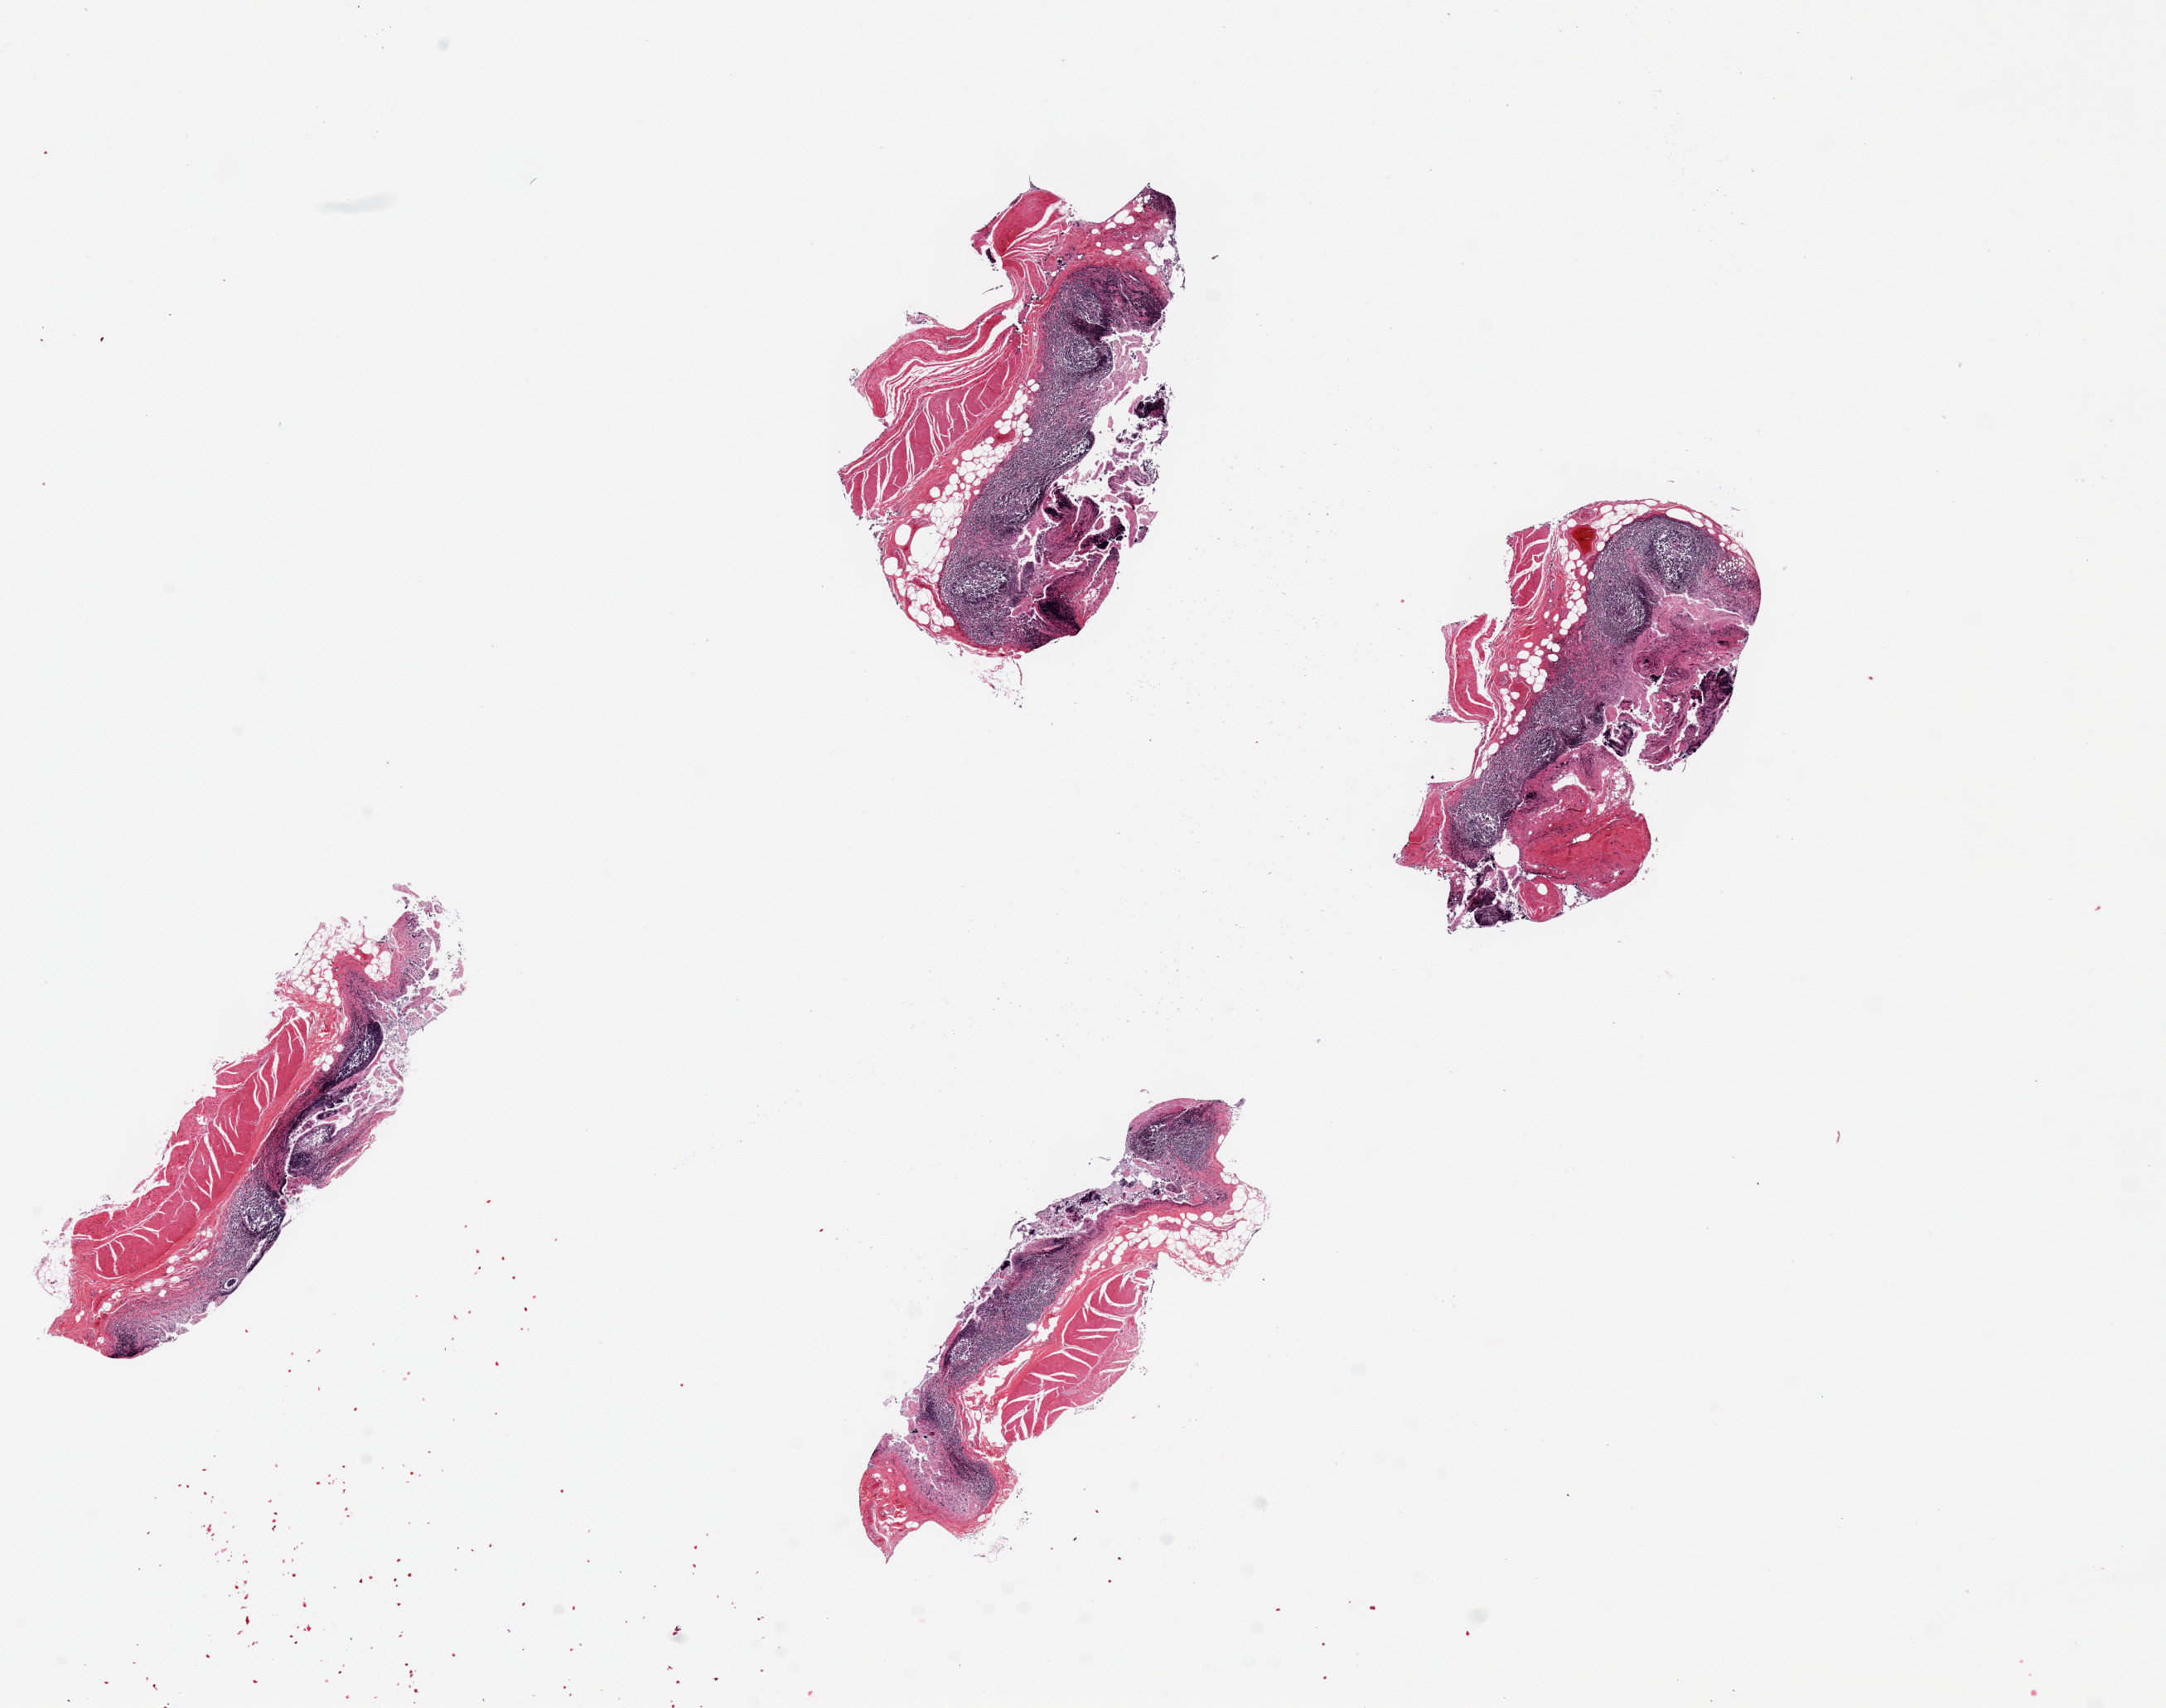
H&E whole-slide image, brightfield, whole scanned area (about 20.7 x 16.3 mm, from a 20x scan) shown as a low-resolution overview, PAXgene-fixed paraffin-embedded (PFPE) section, sampled site (target tissue): ileum, tissue donor sample. Male donor.
* pathologist's review note for this sample: 4 pieces, up to 6x2mm; abundant lymphoid tissue in autolyzed mucosa, but all 4 pieces have muscularis propria